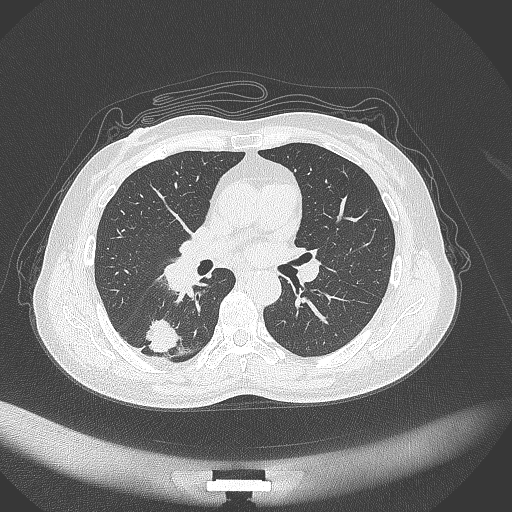
Chest CT, one axial slice; slice 166 of 352 in the series (ordered by position); 120 kVp; lung window (W 1500 / L -600 HU); 512 × 512 image matrix, field of view 400 × 400 mm. Patient: female, 55 years. From the clinical record (not read from this slice): clinical TNM (as recorded): T1c N1 M0.
Outlined on this slice (rectangle marked by the reading radiologist):
- lung tumour (recorded histology: adenocarcinoma): bounding box [x1, y1, x2, y2] px = [141, 314, 180, 357]